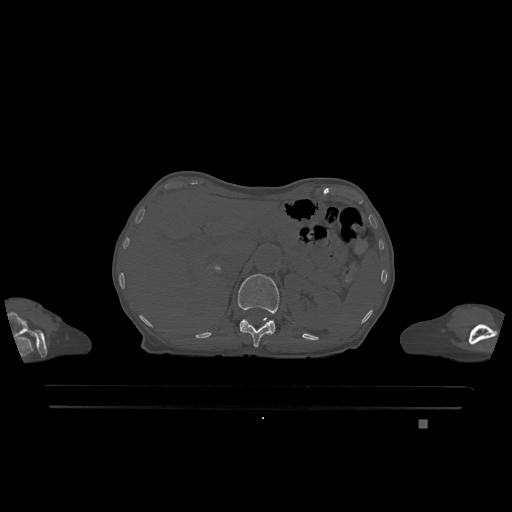
CT including the spine, one axial slice. Position 502 of 1317 along the scan axis. Bone window (W 1800 / L 400 HU). 0.5 mm slice thickness. 512 × 512 image matrix, field of view 500 × 500 mm. Female patient, age 74 years. Case-level facts recorded for this patient, not image findings: primary cancer: lung.
Outlined on this slice (semi-automatically segmented with operator editing):
- L1 vertebra: bounding box <238,274,279,334> (left, top, right, bottom; pixels)
- T12 vertebra: <241,318,272,347>